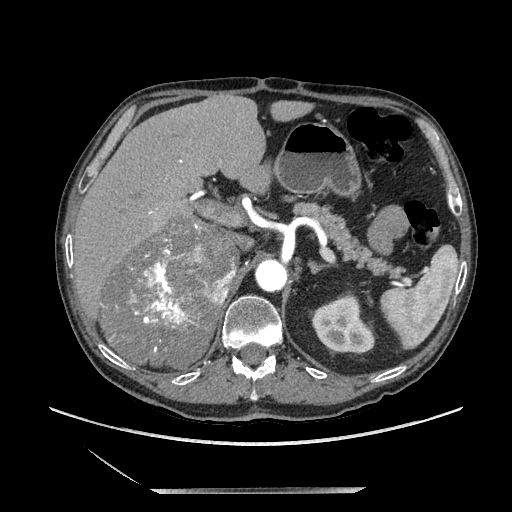
Contrast-enhanced abdominal CT, one axial slice; position 137 of 243 along the scan axis; soft-tissue window (W 400 / L 40 HU); 1.25 mm slice thickness; 512 × 512 image matrix. Male patient. Case-level facts recorded for this patient, not image findings: diagnosis: adrenocortical carcinoma; tumour side: right adrenal; tumour size at pathology: 16 cm; Ki-67 index: 17 %; stage (as recorded): 3.
Structures marked on this image (semi-automatic segmentation, software-assisted and operator-edited):
- mass: bounding box <103,223,237,367> (left, top, right, bottom; pixels)